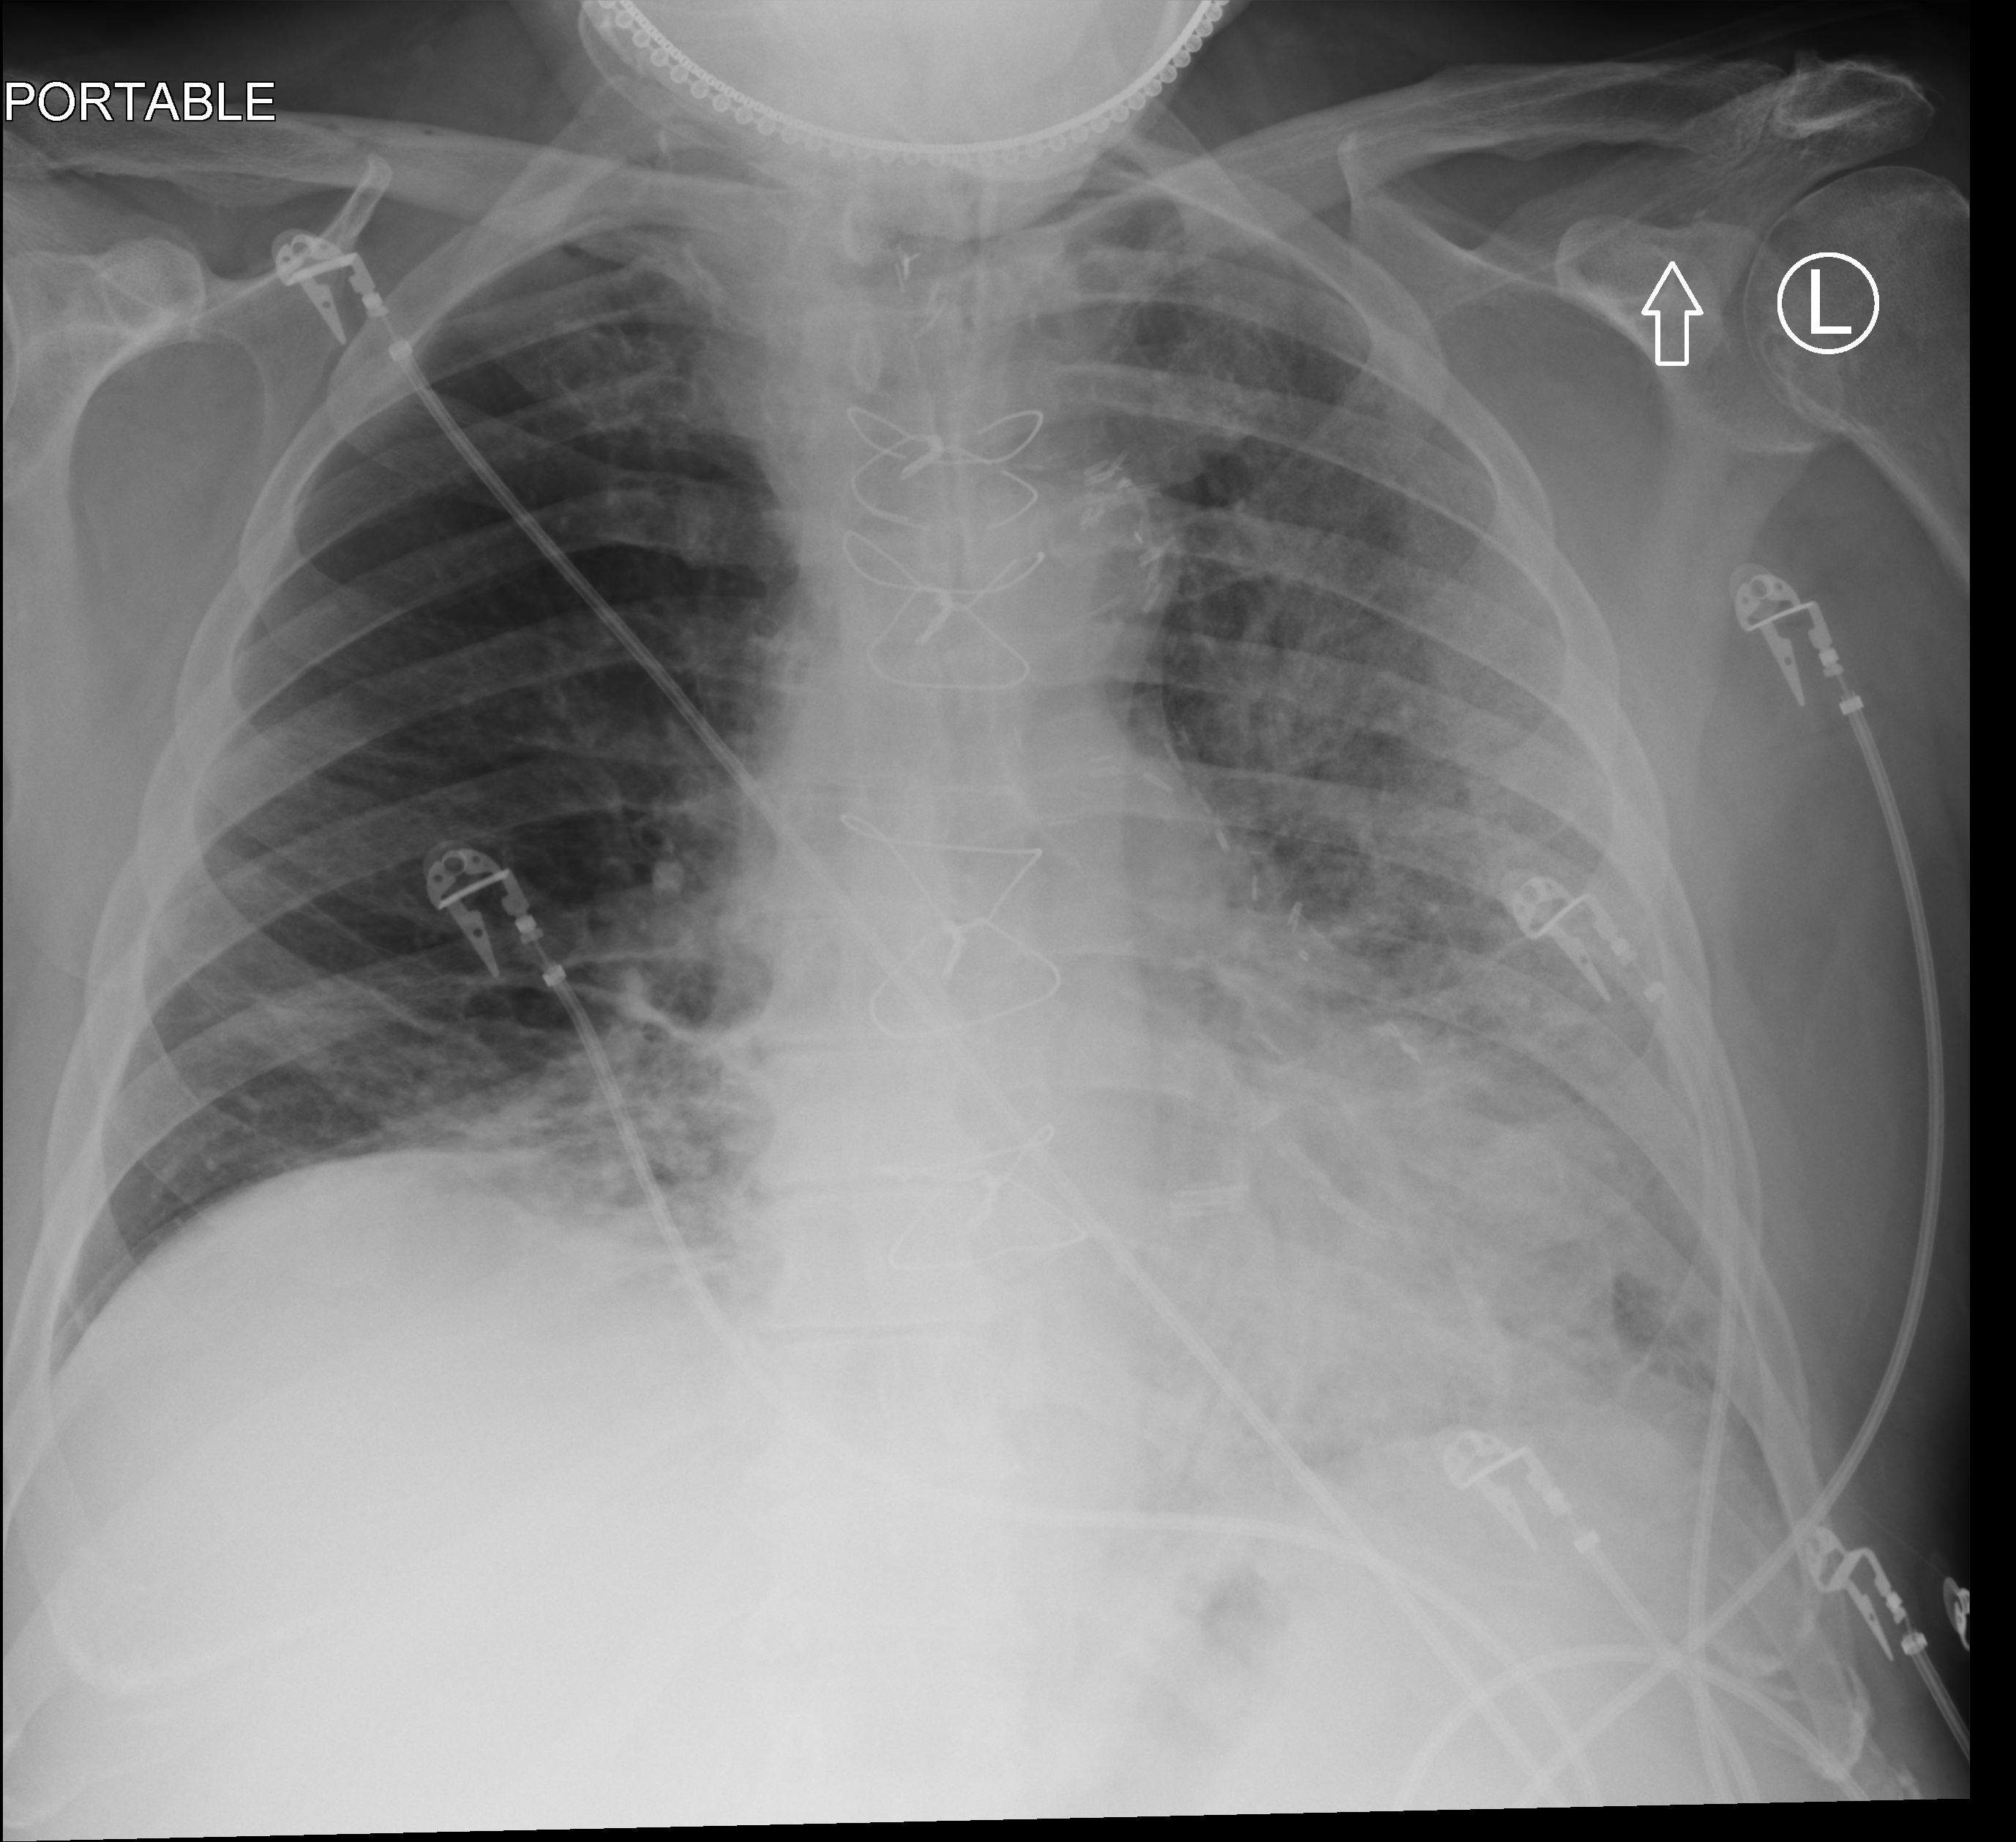
Bedside chest radiograph (computed radiography), anteroposterior (AP) projection. Male patient hospitalised with COVID-19, age 60–74 years.
Admission-level facts for this patient (not findings on this image; timing relative to this image not recorded): other chronic lung disease (admission record): no.